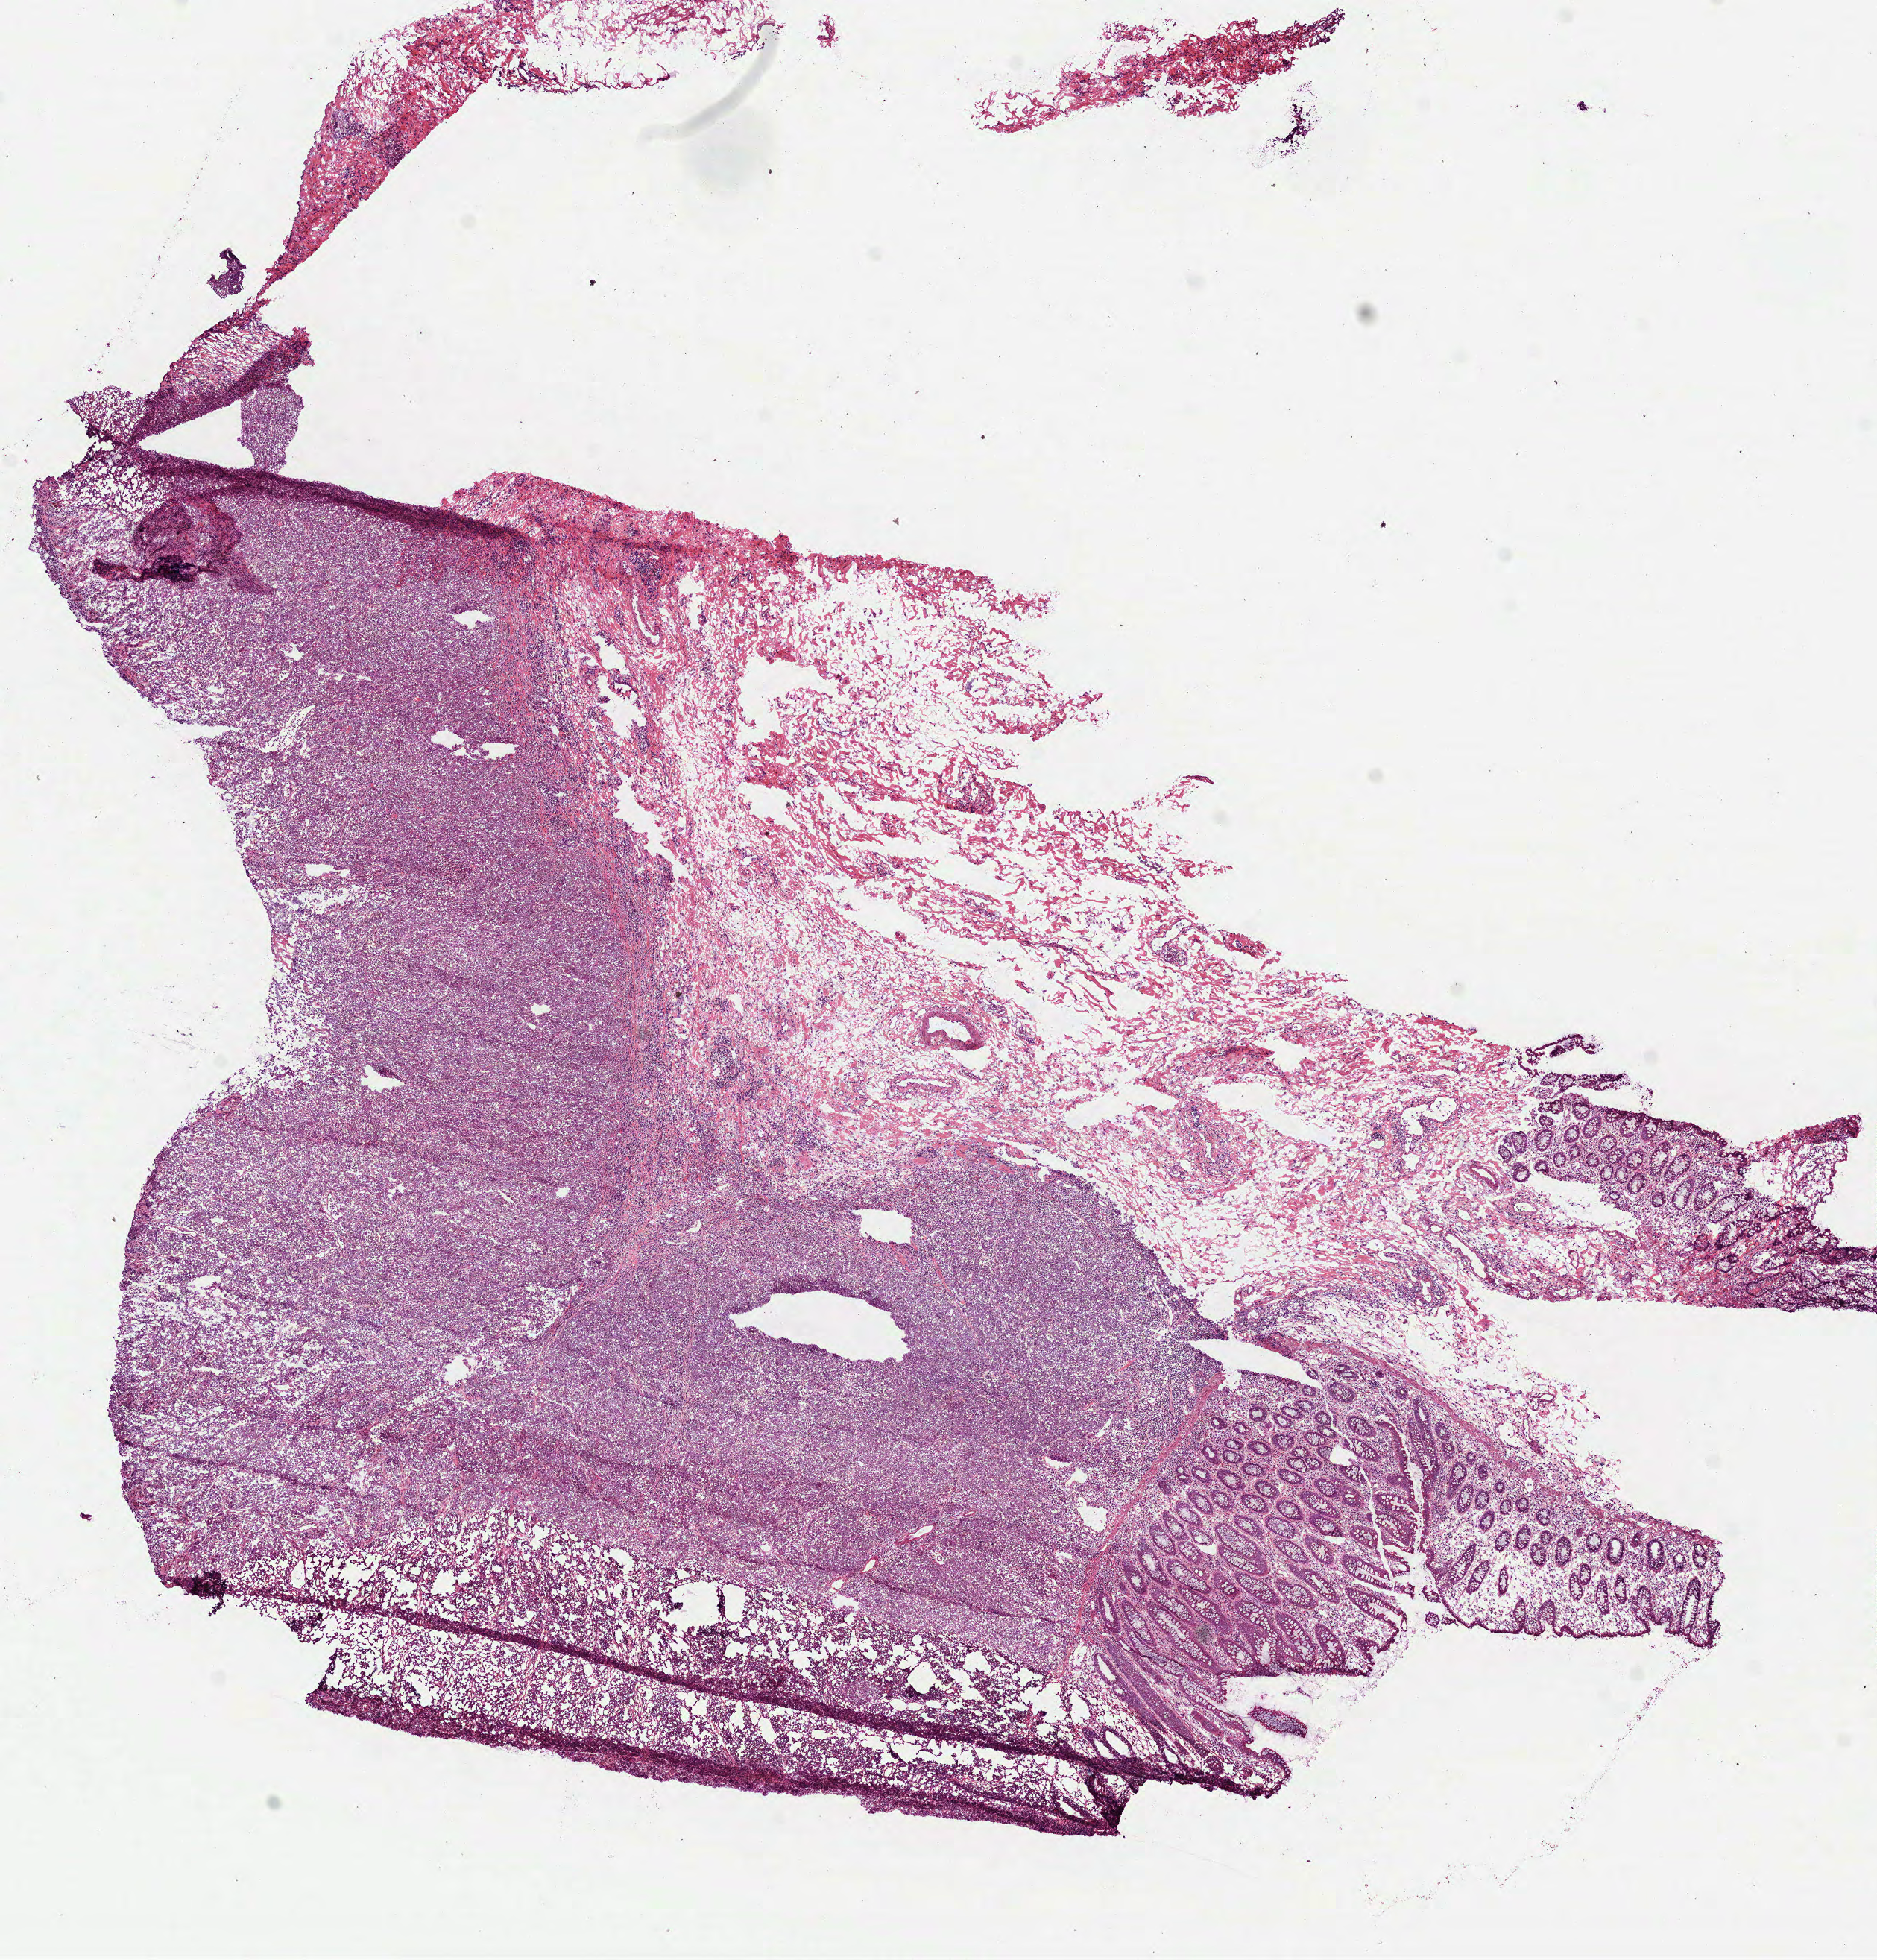
Whole-slide histology image, Hematoxylin and eosin (H&E) stained, a low-resolution overview of the entire scanned area, about 10.2 x 10.6 mm (acquisition: 40x scan), frozen section, primary tumour sample from the colon. Male patient; age at initial diagnosis 78 years. Composition of this section per pathologist review: tumour cells 75%, tumour nuclei 75%, normal cells 10%, stromal cells 15%, necrosis 0%.
- lymph nodes positive (case pathology): 0 of 16 examined
- AJCC pathologic stage: I
- histologic diagnosis: Adenocarcinoma, NOS (cecum)